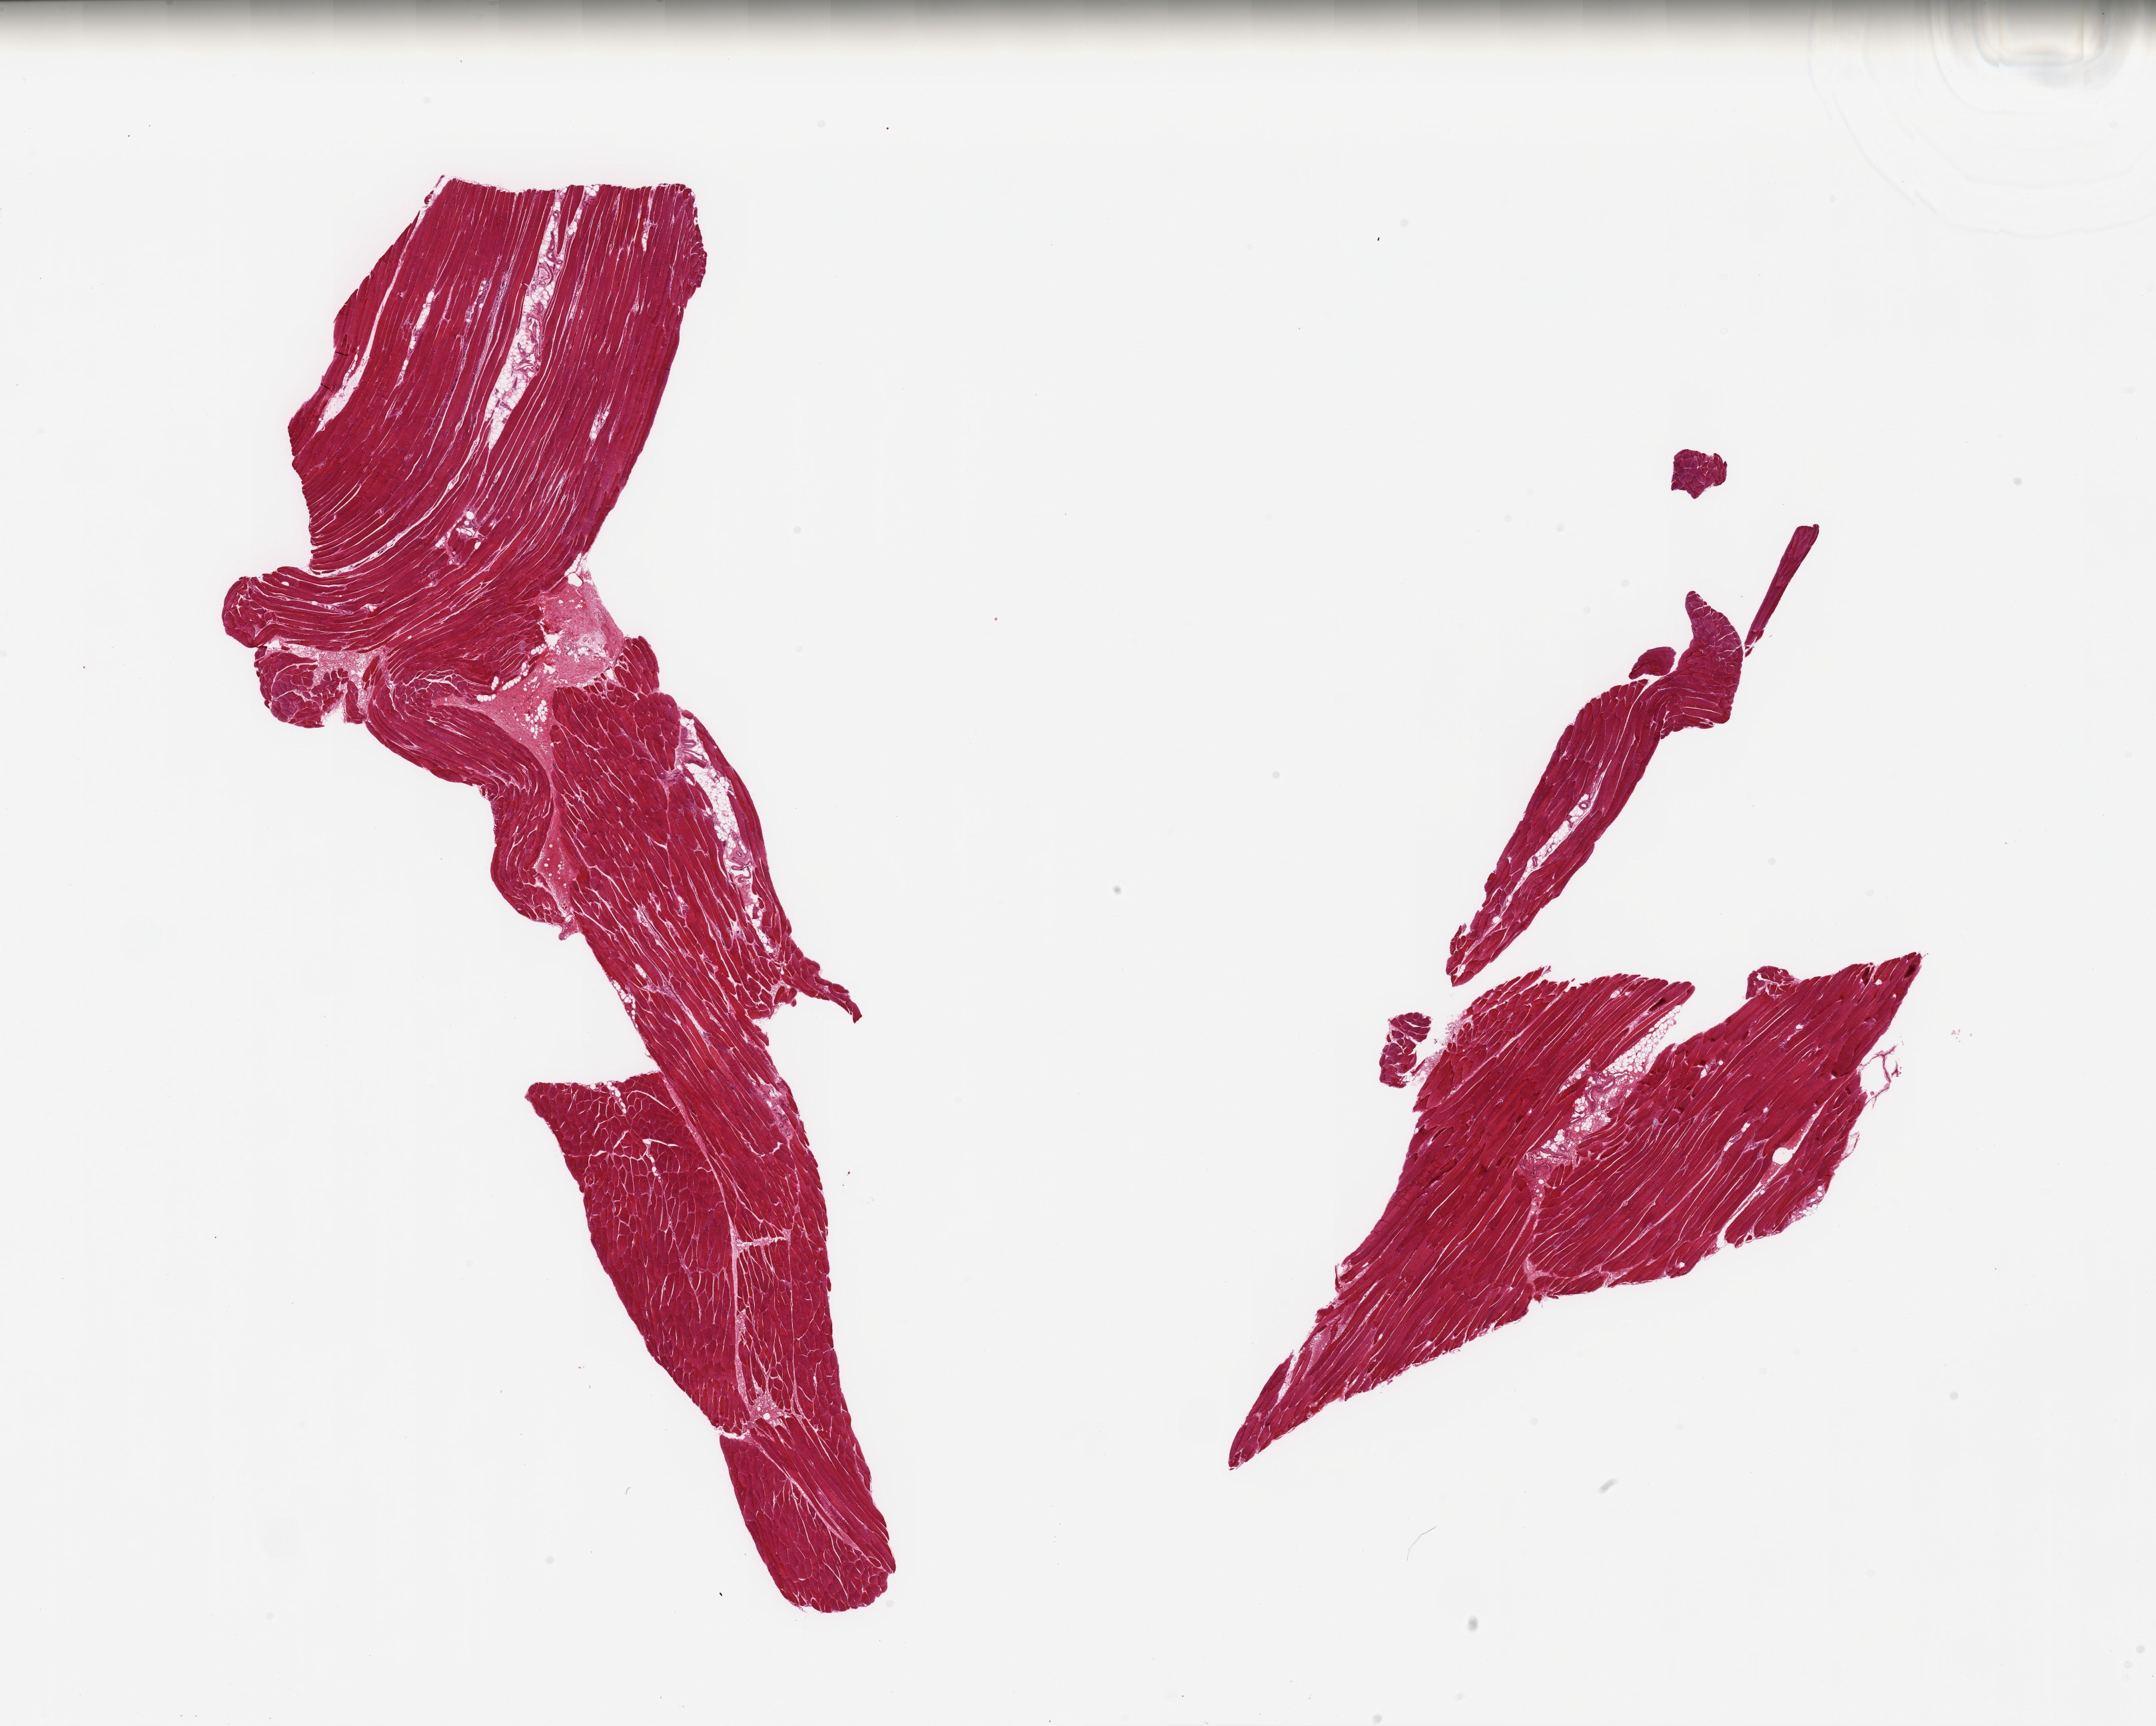
Whole-slide image, haematoxylin and eosin stain, brightfield, low-resolution overview of the scanned area, about 25.6 x 20.5 mm (slide scanned at 20x), PAXgene-fixed, paraffin-embedded tissue, section of skeletal muscle (target tissue), donor tissue sample. Male donor.
Review note (as recorded): 2 pieces; 5% internal fat.